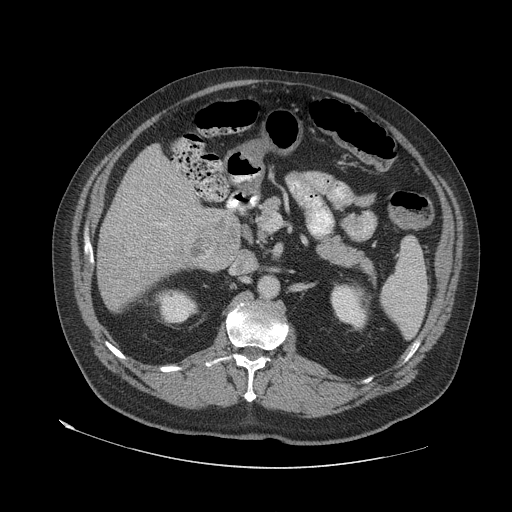
Contrast-enhanced abdominal CT (liver protocol), one axial slice; position 26 of 79 along the scan axis; reconstruction kernel STANDARD; soft-tissue window (W 400 / L 40 HU); 512 × 512 image matrix, field of view 480 × 480 mm. From the clinical record (not read from this slice): diagnosis: hepatocellular carcinoma (patient treated with transarterial chemoembolisation; whether this scan precedes or follows treatment is not stated here); TNM stage (as recorded): Stage-IVA; Child-Pugh class: A; tumour nodularity: multinodular.
Annotated regions visible in this slice (semi-automatically segmented with operator editing):
- liver parenchyma outside the tumour (the mass and vessels are separate outlines, so this box may not span the whole liver): bounding box [x1, y1, x2, y2] px = [98, 144, 218, 310]
- liver vessels: [159, 224, 166, 226]